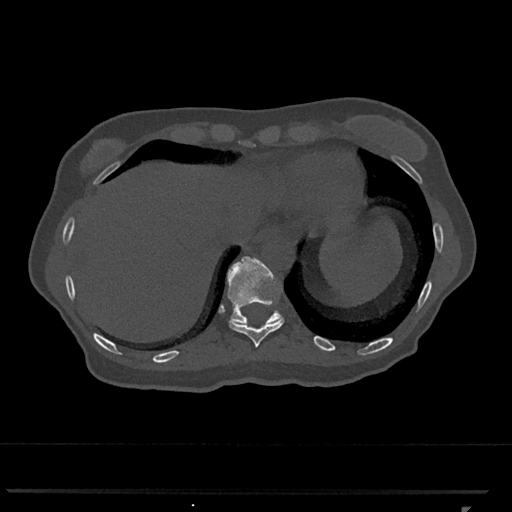
CT including the spine, one axial slice. Slice 552 of 793 in the series (ordered by position). Reconstruction kernel Br40s/3. 120 kVp. Bone window (W 1800 / L 400 HU). 0.5 mm slice thickness. 512 × 512 image matrix. Female patient, age 62 years. Case-level facts recorded for this patient, not image findings: primary cancer: renal.
Structures marked on this image (semi-automatic segmentation, software-assisted and operator-edited):
- T10 vertebra: bounding box [x1, y1, x2, y2] px = [229, 318, 285, 347]
- T11 vertebra: [227, 256, 283, 325]